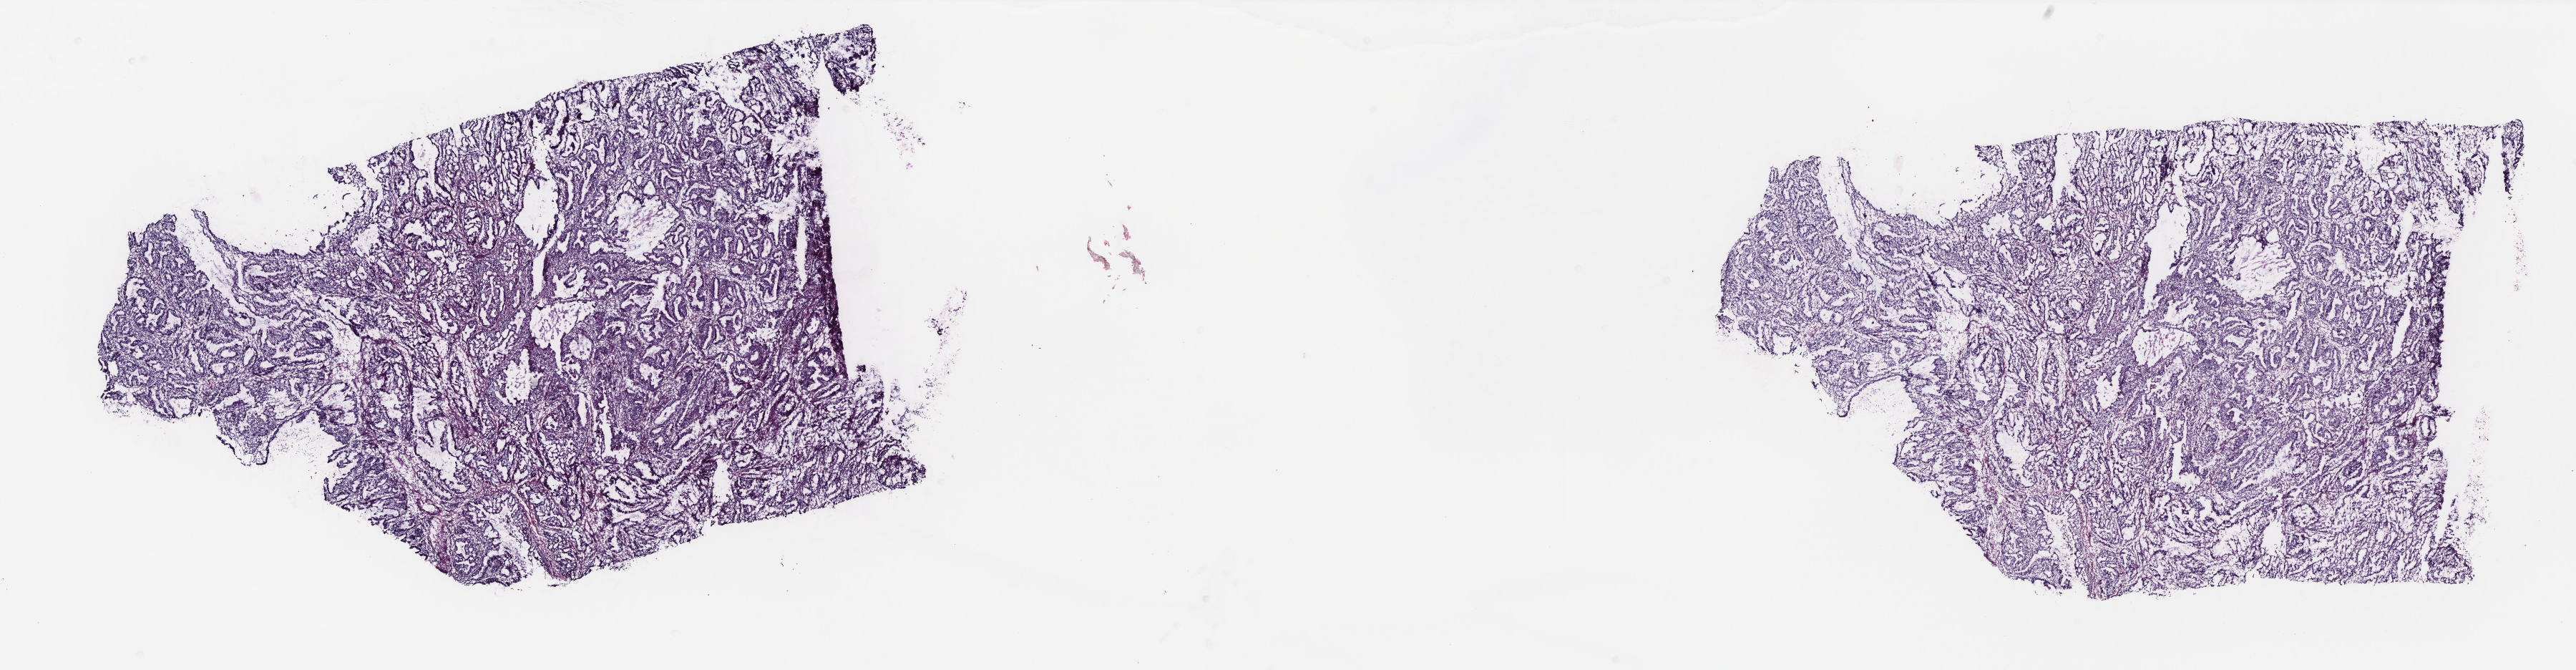
Whole-slide histology image, H&E-stained — a low-resolution overview of the entire scanned area, about 28.9 x 7.5 mm (from a 40x scan), frozen section from the top of the tissue portion, sample: primary tumour, uterus. Female, age 74 years at initial diagnosis.
Pathologic diagnosis: Endometrioid adenocarcinoma, NOS (endometrium).